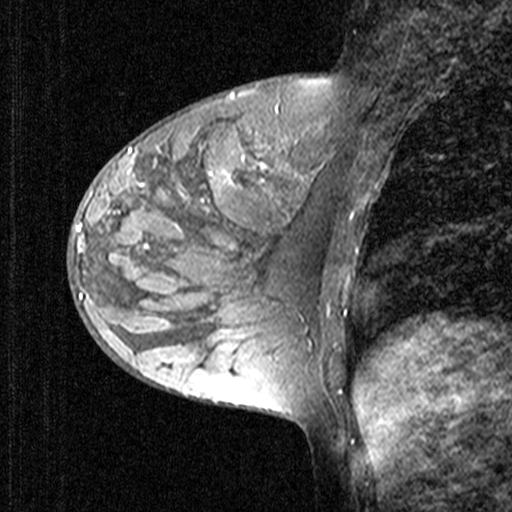
Breast MRI (dynamic contrast-enhanced), one sagittal slice; position 17 of 44 along the scan axis; dynamic contrast-enhanced study with each time point stored as its own series, time point 2 of 3 at this slice position (early post-contrast, ordered by acquisition time); 1.5 T; TE 4.5 ms, TR 11 ms; 3 mm slice thickness; 512 × 512 image matrix. Female patient, age 27 years. From the clinical record (not read from this slice): setting: breast cancer imaged before/during neoadjuvant chemotherapy; receptor status: HR-positive, HER2-negative.
Structures marked on this image (semi-automatically segmented with operator editing):
- analysis volume of interest (the breast-tissue region the enhancement analysis was run in; not a lesion): box from (x=69, y=146) to (x=165, y=239) px
- tumour enhancement mask (voxels above the 90 % enhancement threshold inside the analysis volume of interest): (x=74, y=147)–(x=133, y=235)